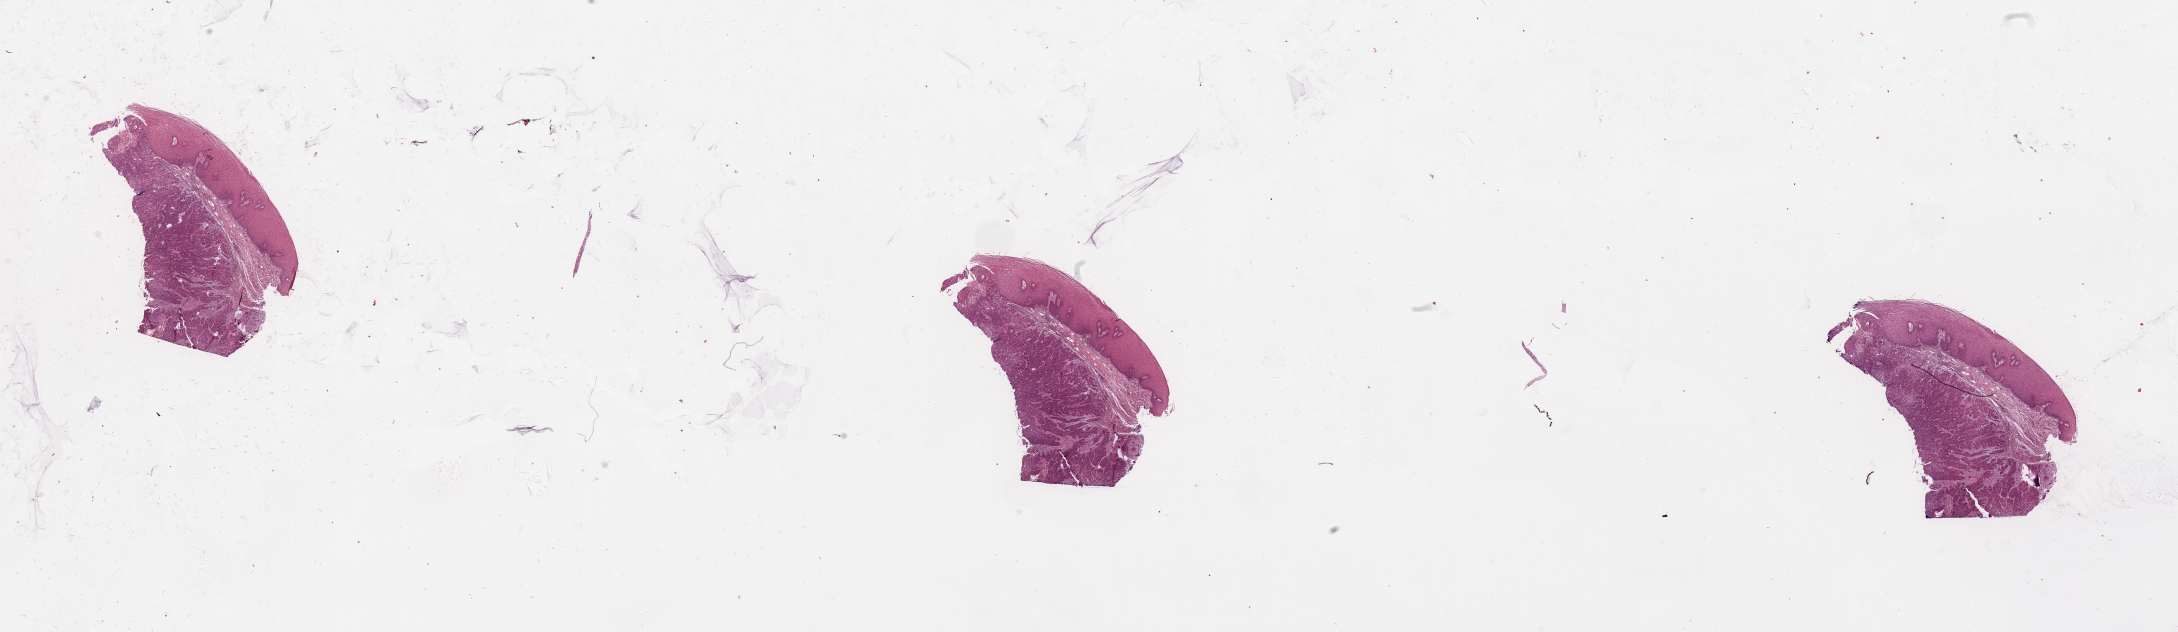
Digitized H&E tissue section (whole slide) — low-resolution overview of the scanned area, about 34.5 x 10.0 mm. Head and neck, tissue type not recorded. 68-year-old female patient.
Patient diagnosis: Squamous cell carcinoma, NOS (larynx, NOS).